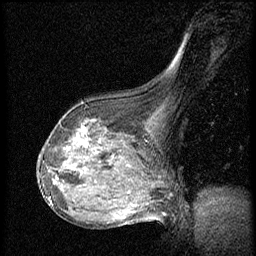
Breast MRI (dynamic contrast-enhanced), one sagittal slice. Position 38 of 56 along the scan axis. Dynamic contrast-enhanced series, image 2 of 3 at this slice position (ordered by acquisition). 1.5 T. TE 4.2 ms, TR 20.4 ms. 2 mm slice thickness. 256 × 256 image matrix, field of view 200 × 200 mm. Female patient, age 64 years. From the clinical record (not read from this slice): setting: breast cancer imaged before/during neoadjuvant chemotherapy; receptor status: HR-positive, HER2-negative.
Outlined on this slice (semi-automatically segmented with operator editing):
- analysis volume of interest (the breast-tissue region the enhancement analysis was run in; not a lesion): bounding box [x1, y1, x2, y2] px = [48, 101, 142, 186]
- tumour enhancement mask (voxels above the 70 % enhancement threshold inside the analysis volume of interest): [78, 129, 87, 146]